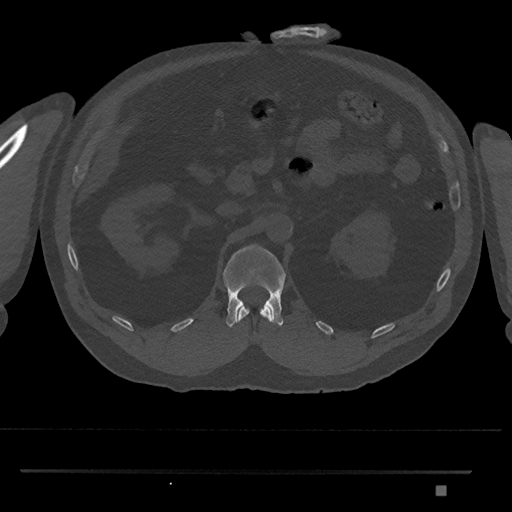
CT including the spine, one axial slice. Slice 845 of 1134 in the series (ordered by position). 120 kVp. Bone window (W 1800 / L 400 HU). 0.5 mm slice thickness. 512 × 512 image matrix. Male patient, age 65 years. From the clinical record (not read from this slice): primary cancer: prostate.
Annotated regions visible in this slice (semi-automatically segmented with operator editing):
- L1 vertebra: bounding box [x1, y1, x2, y2] px = [223, 244, 286, 328]
- T12 vertebra: [237, 305, 272, 323]